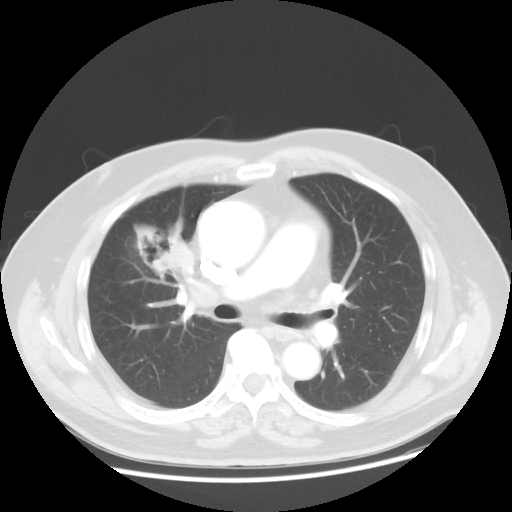
Chest CT, one axial slice; slice 27 of 48 in the series (ordered by position); 120 kVp; lung window (W 1500 / L -600 HU); 512 × 512 image matrix, field of view 392 × 392 mm. Patient: male, 60 years. Case-level facts recorded for this patient, not image findings: clinical TNM (as recorded): T2 N3 M0; histopathological grade: G2-3.
Annotated regions visible in this slice (bounding box drawn by a radiologist):
- lung tumour (recorded histology: adenocarcinoma): bounding box (x1, y1, x2, y2) in pixels: (127, 204, 193, 289)